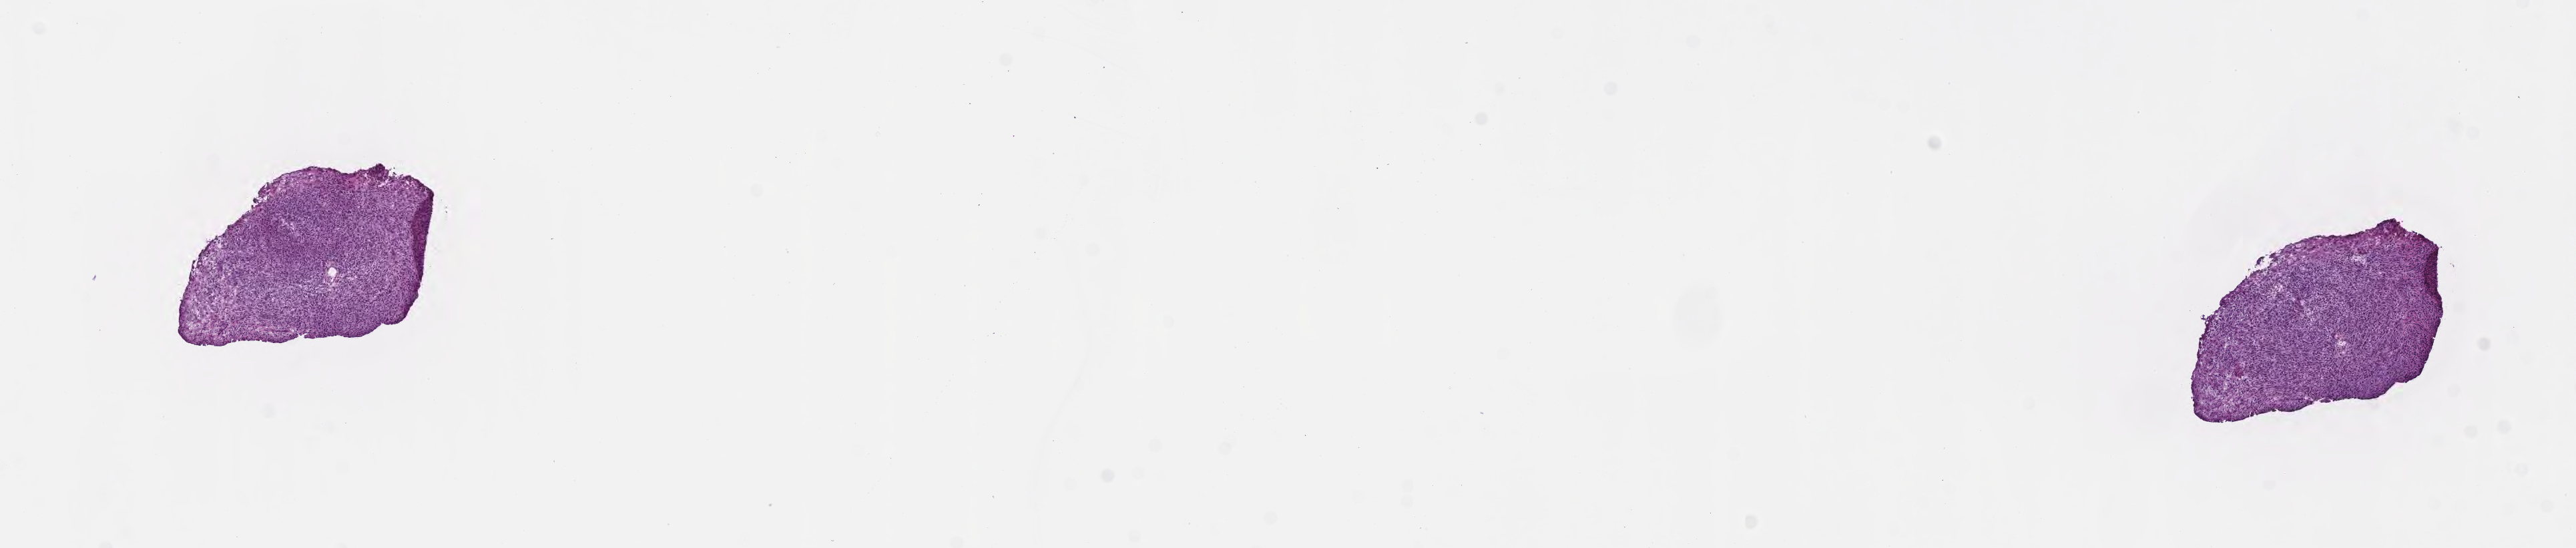
Whole-slide image, H&E stain — whole scanned area (about 15.6 x 3.3 mm) shown as a low-resolution overview; frozen section (tissue freezing medium); specimen: metastatic tumor tissue, resected from brain. Male patient; age at initial diagnosis 31 years. Composition of this section per pathologist review: tumor cells 80%, tumor nuclei 90%, stromal cells 20%, necrosis 0%, normal cells 0%. Inflammatory infiltration, as recorded: lymphocyte infiltration 0%, monocyte infiltration 0%, neutrophil infiltration 0%.
- section: top of the tissue portion
- patient diagnosis (primary): Malignant melanoma, NOS